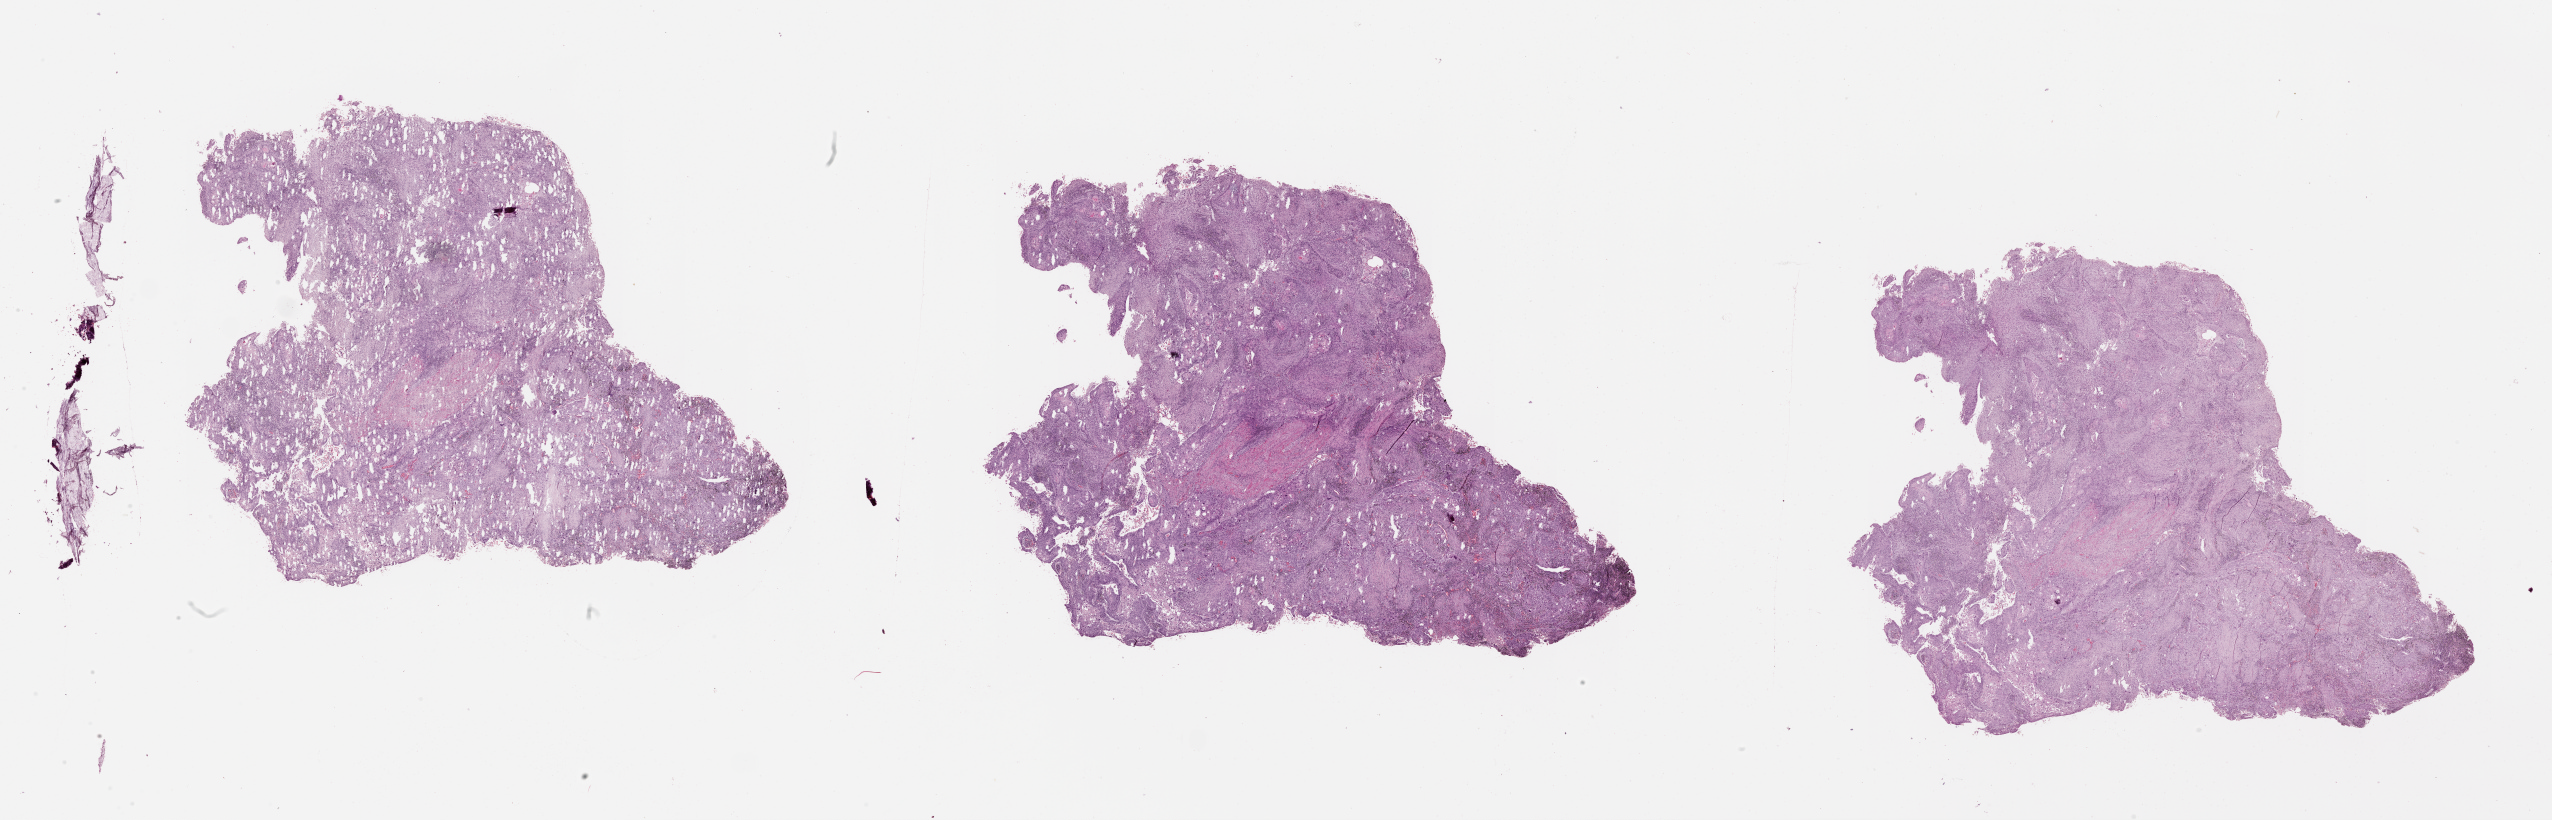
Digitized H&E-stained tissue section (whole slide), a low-resolution overview of the entire scanned area, about 41.1 x 13.2 mm (slide scanned at 20x); lung, tumour tissue. 68-year-old male patient.
Patient diagnosis (cohort enrolment): squamous cell carcinoma (lung).